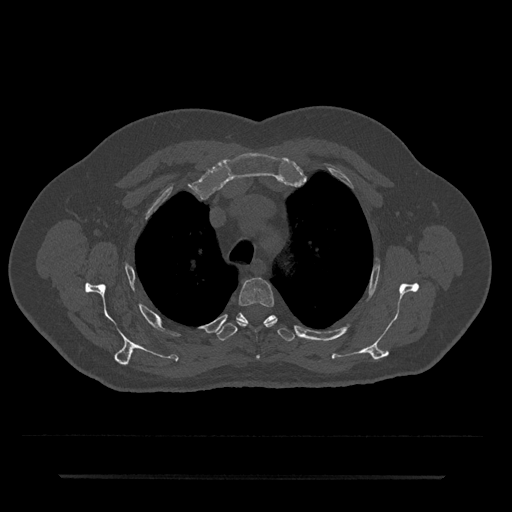
CT including the spine, one axial slice; position 552 of 797 along the scan axis; 120 kVp; bone window (W 1800 / L 400 HU); 0.5 mm slice thickness; 512 × 512 image matrix, field of view 437 × 437 mm. Male patient, age 69 years. Case-level facts recorded for this patient, not image findings: primary cancer: prostate.
Structures marked on this image (semi-automatic segmentation, software-assisted and operator-edited):
- T3 vertebra: bounding box (x1, y1, x2, y2) in pixels: (236, 277, 277, 359)
- T4 vertebra: (216, 313, 295, 342)